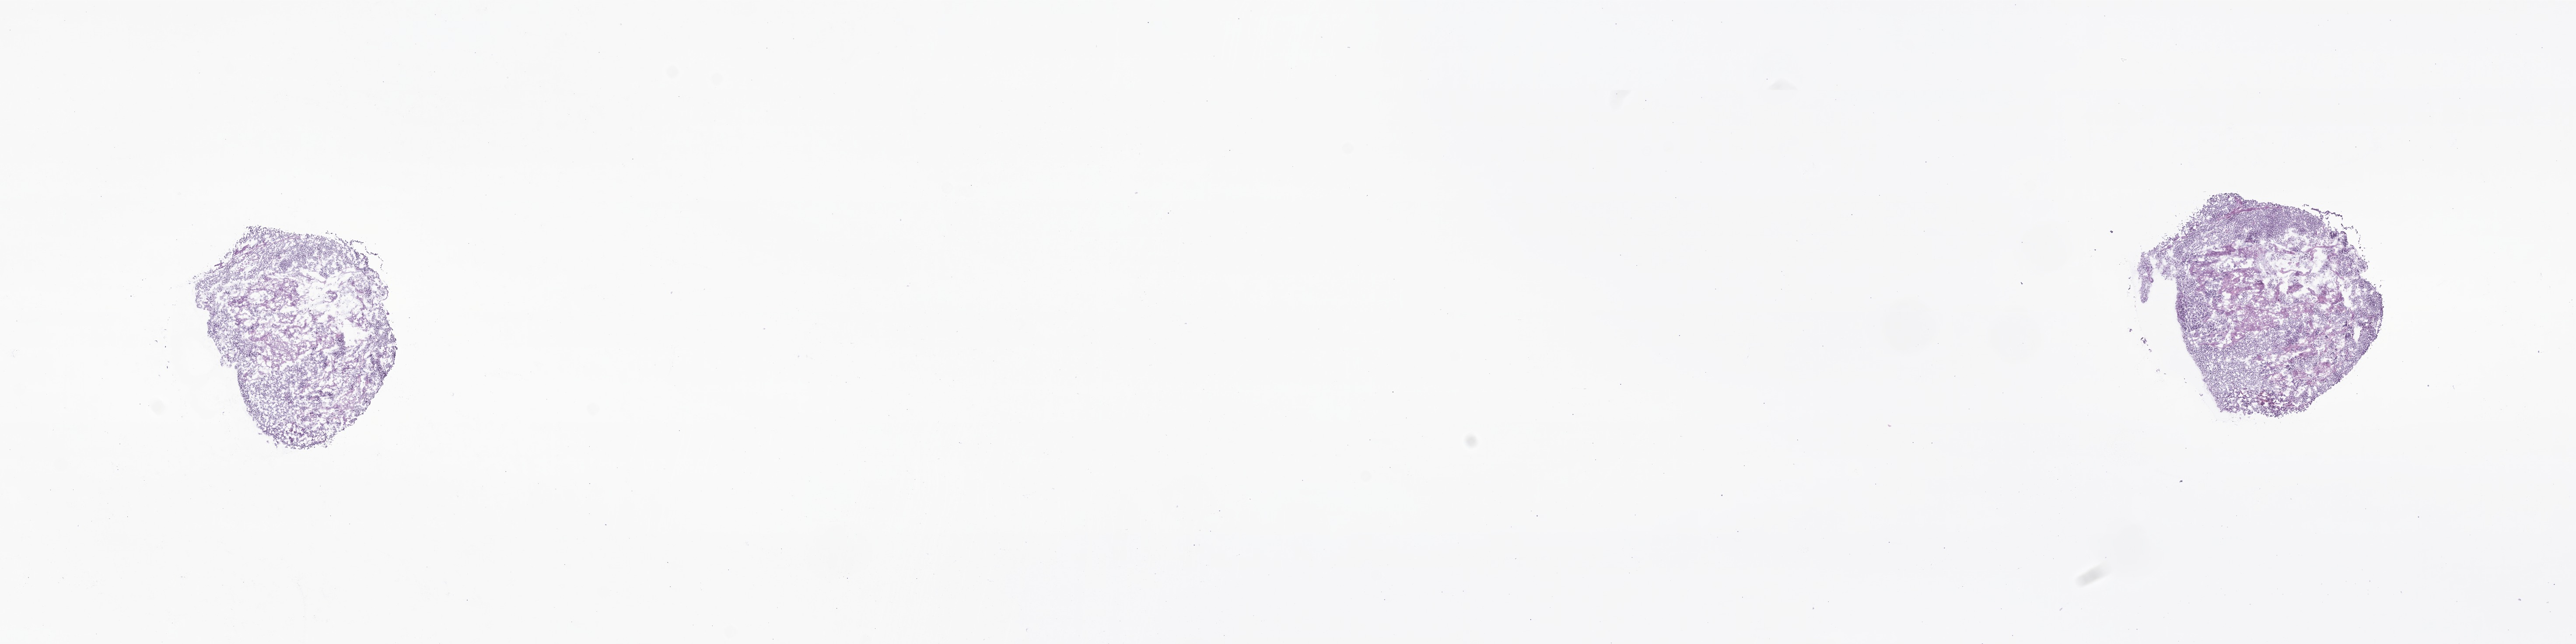
Digitized H&E-stained section of tumor tissue from the brain — low-resolution overview of the scanned area, about 24.8 x 6.2 mm. Cryosection (OCT / tissue freezing medium). Patient: female, age 182 months (15 years 2 months).
Diagnosis (ICD-O-3 morphology term): Neoplasm, uncertain whether benign or malignant.